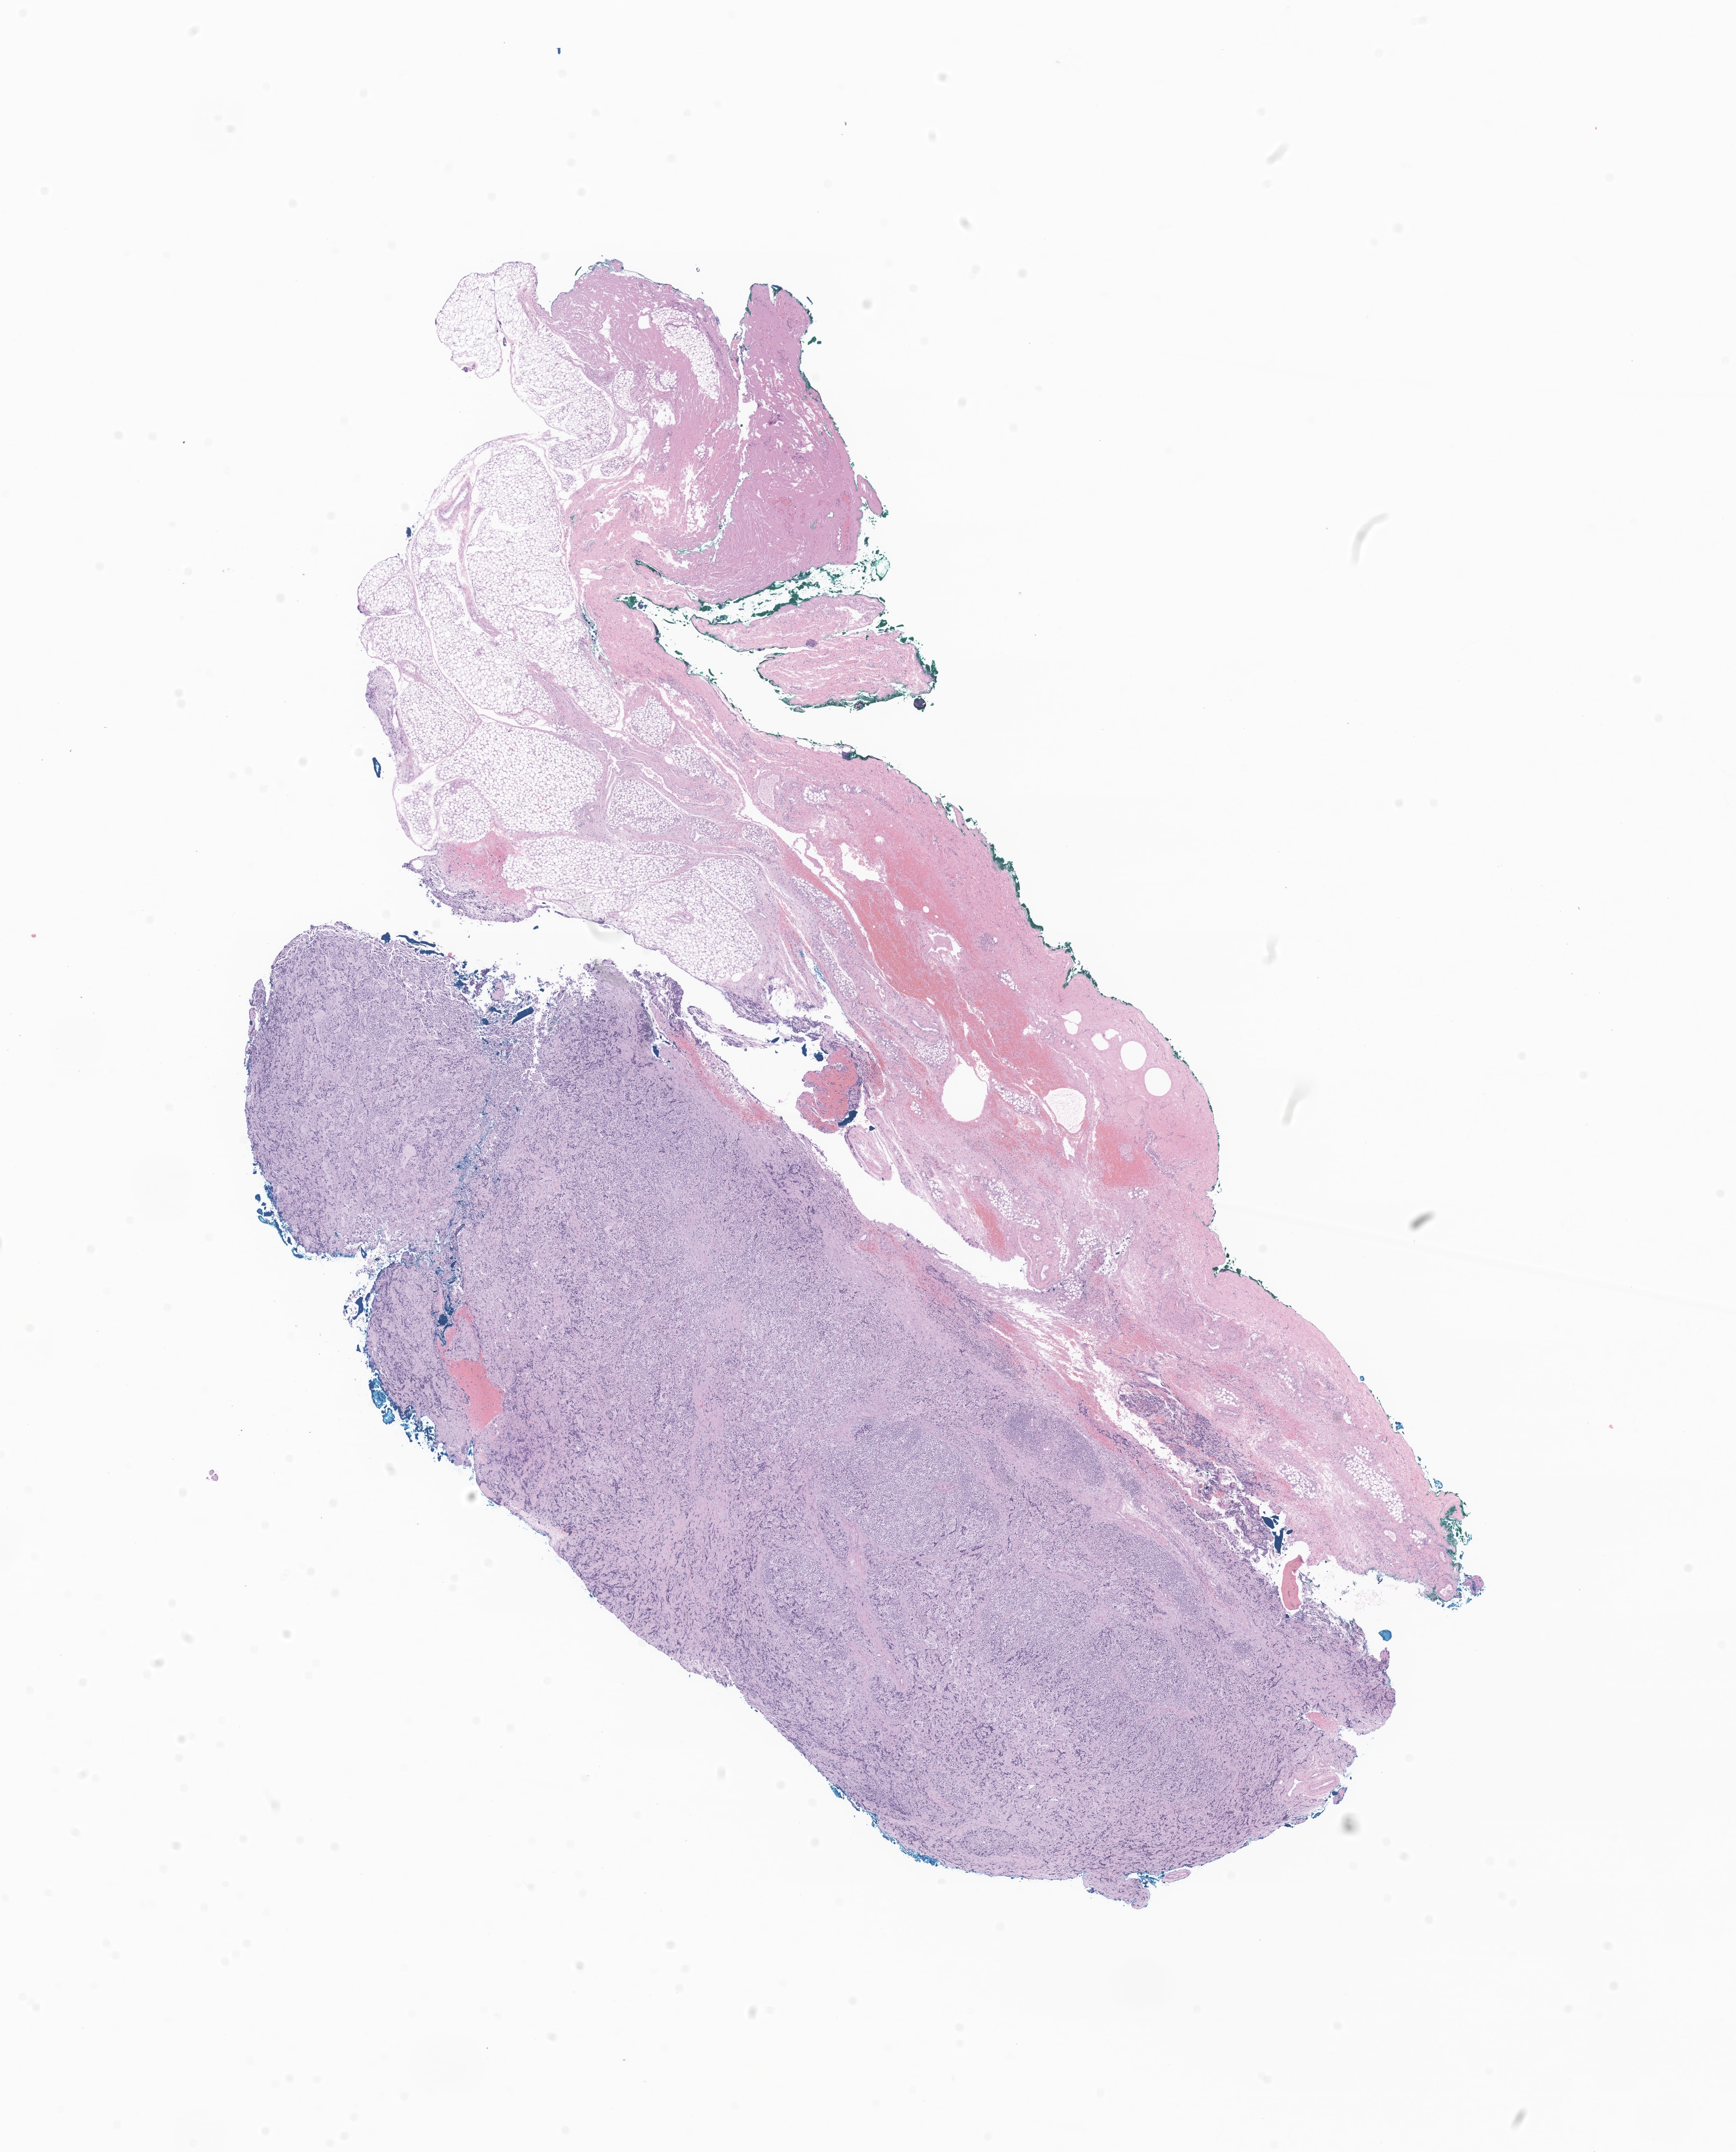
Whole-slide image, H&E stain of tumor tissue from the adrenal gland — low-resolution overview of the scanned area, about 13.6 x 16.9 mm, formalin-fixed paraffin-embedded section. Female patient, age 421 days (about 1.2 years).
Recorded diagnosis: Neuroblastoma, NOS.